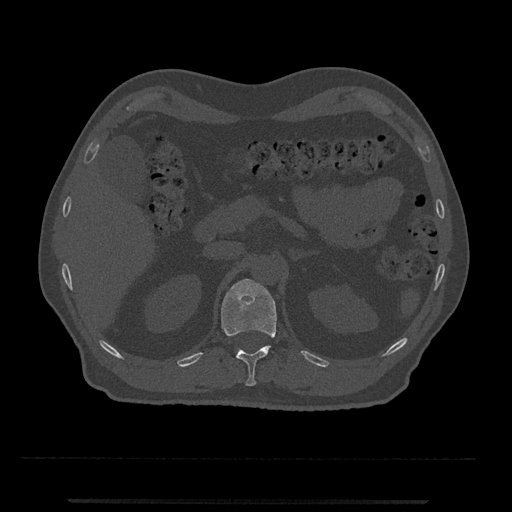
CT including the spine, one axial slice; slice 390 of 797 in the series (ordered by position); reconstruction kernel Br40s/3; bone window (W 1800 / L 400 HU); 0.5 mm slice thickness; 512 × 512 image matrix. Patient: male, 63 years. Case-level facts recorded for this patient, not image findings: primary cancer: prostate.
Annotated regions visible in this slice (semi-automatic segmentation, software-assisted and operator-edited):
- T12 vertebra: bounding box <221,279,277,386> (left, top, right, bottom; pixels)